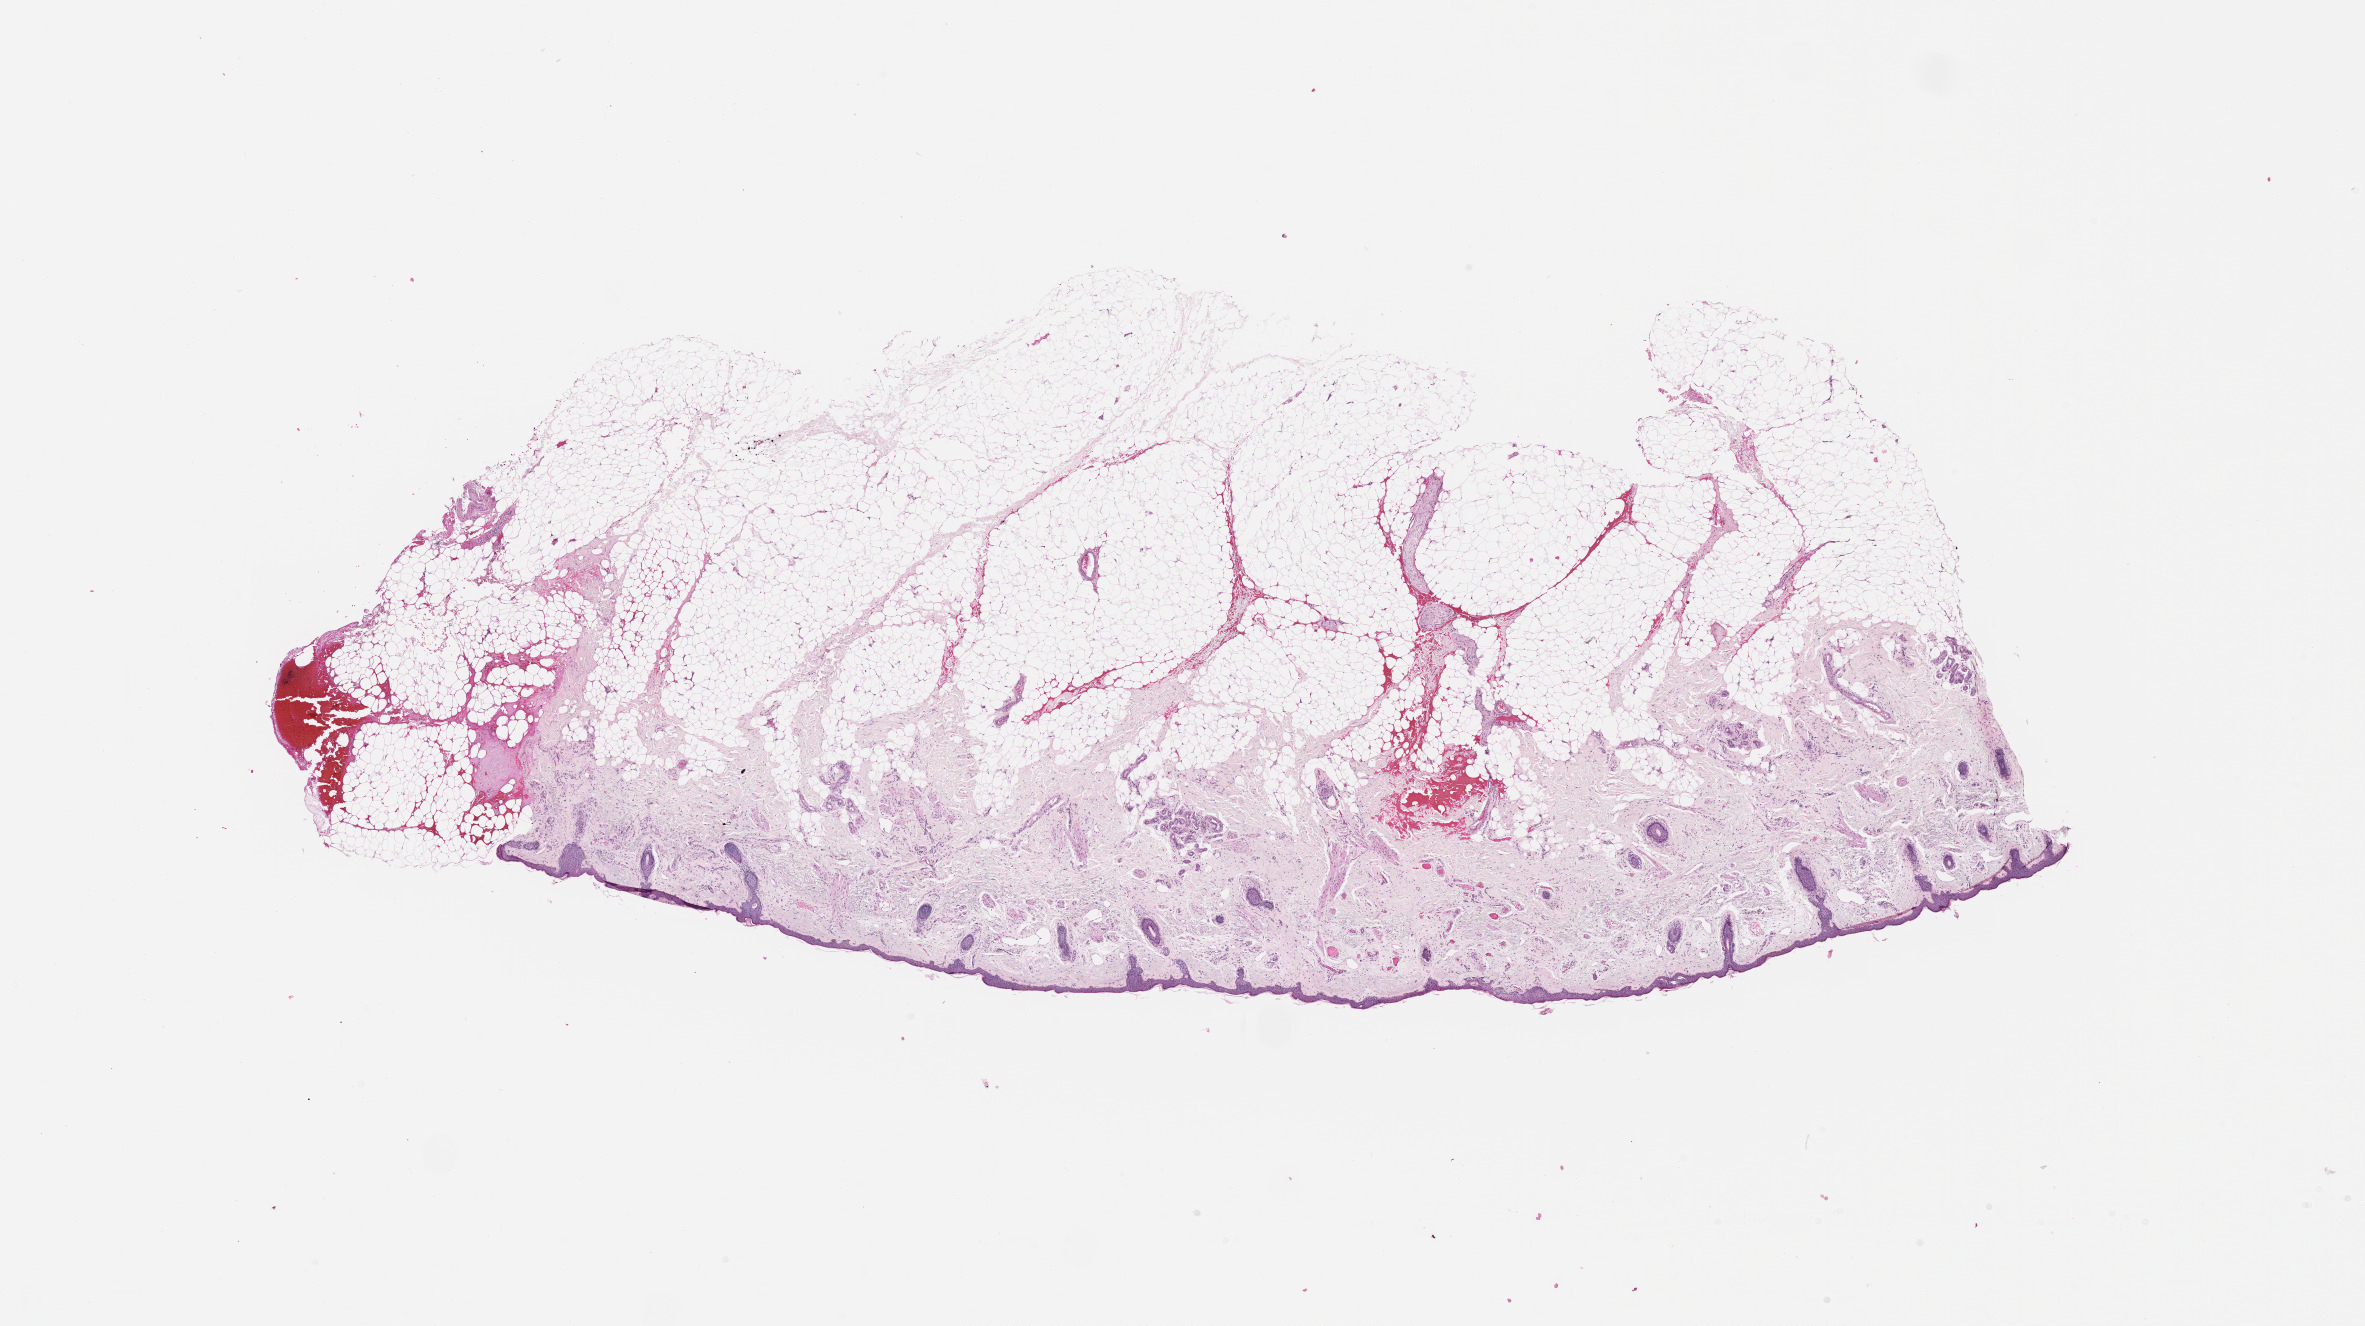
Digitized H&E tissue section (whole slide) — low-resolution overview of the scanned area, about 19.0 x 10.7 mm; normal (non-tumour) tissue sample, sampled site: head & neck. Patient: female, age 82 years.
This section: normal (non-tumour) tissue from the same patient. Patient diagnosis: Malignant melanoma, NOS.